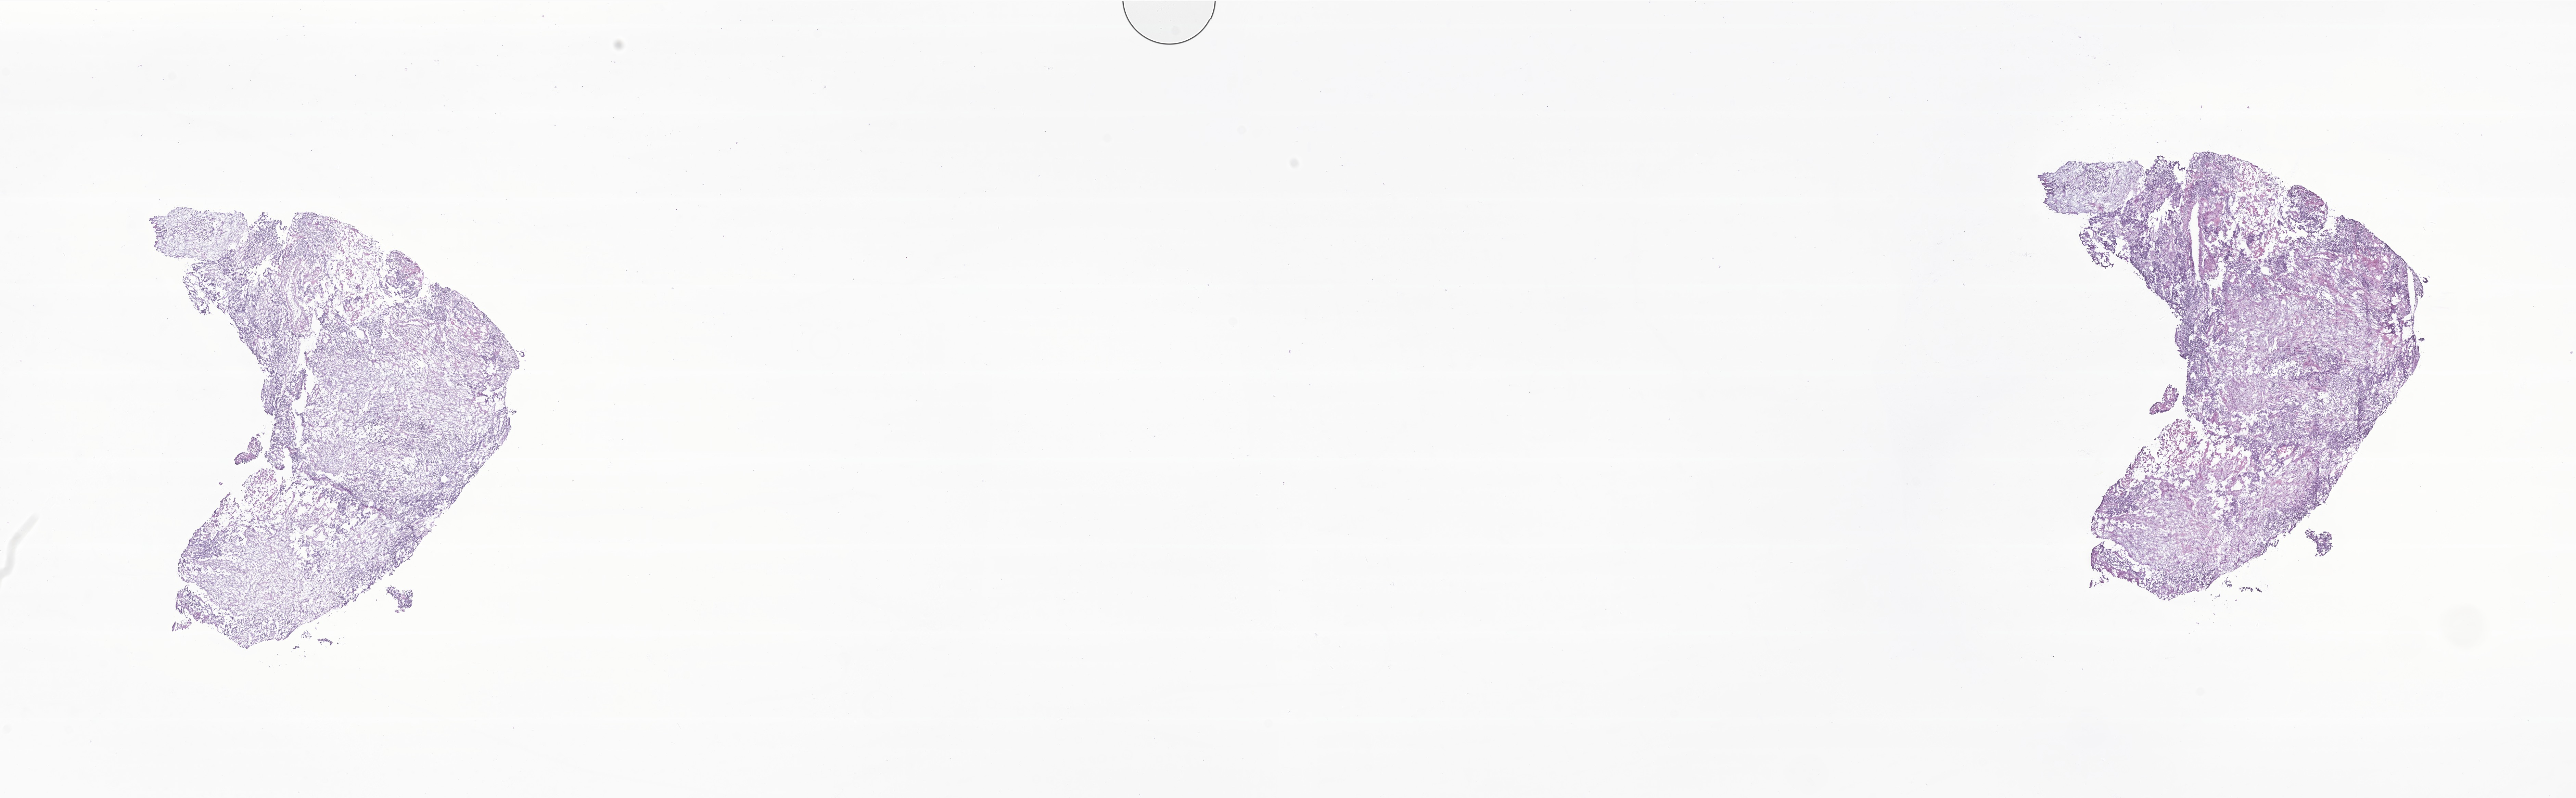
Digitized H&E-stained section of tumor tissue from the abdomen, whole scanned area (about 31.7 x 9.8 mm) shown as a low-resolution overview. Frozen section. Patient: male, age 102 months (8 years 6 months).
- recorded diagnosis: Rhabdomyosarcoma, NOS